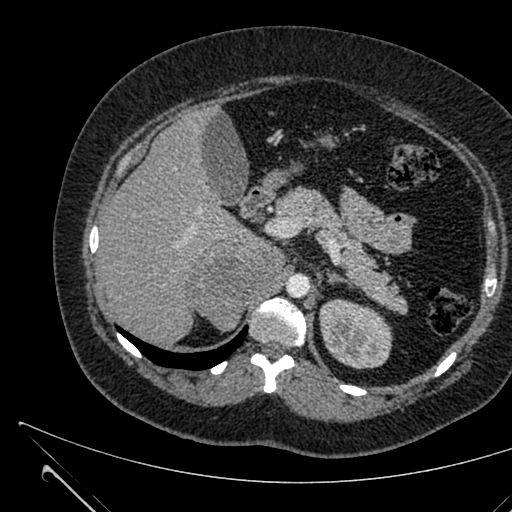
Contrast-enhanced abdominal CT, one axial slice; slice 433 of 731 in the series (ordered by position); 120 kVp; intravenous contrast given; soft-tissue window (W 400 / L 40 HU); 1 mm slice thickness; 512 × 512 image matrix, field of view 376 × 376 mm. Patient: female, 36 years. Case-level facts recorded for this patient, not image findings: diagnosis: adrenocortical carcinoma; tumour side: right adrenal; tumour size at pathology: 10 cm; Ki-67 index: 20 %; stage (as recorded): 4.
Annotated regions visible in this slice (semi-automatic segmentation, software-assisted and operator-edited):
- mass: bounding box [x1, y1, x2, y2] px = [191, 243, 283, 331]